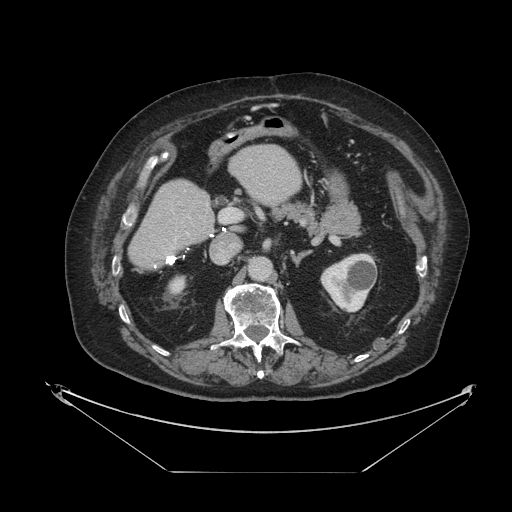
Contrast-enhanced abdominal CT, one axial slice; position 48 of 121 along the scan axis; reconstruction kernel STANDARD; 120 kVp; intravenous contrast given; soft-tissue window (W 400 / L 40 HU); 2.5 mm slice thickness; 512 × 512 image matrix. Male patient, age 68 years. From the clinical record (not read from this slice): diagnosis: colorectal cancer liver metastases, imaged before liver resection; multiple liver metastases: no; largest metastasis: 4 cm; disease in both lobes: no.
Structures marked on this image (manually delineated by an expert):
- hepatic veins: bounding box [x1, y1, x2, y2] px = [165, 257, 167, 259]
- liver: [130, 146, 301, 269]
- planned liver remnant (the part of the liver to remain after resection): [130, 146, 301, 269]
- portal vein (with intrahepatic branches): [182, 208, 237, 235]